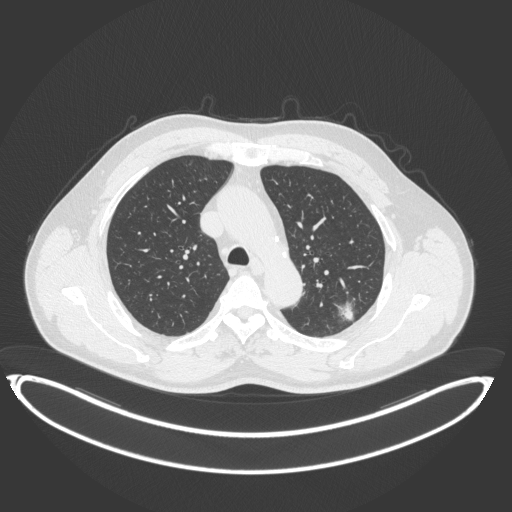
Chest CT, one axial slice; position 261 of 399 along the scan axis; reconstruction kernel B31f; 120 kVp; lung window (W 1500 / L -600 HU); 1 mm slice thickness; 512 × 512 image matrix. Male patient, age 58 years. From the clinical record (not read from this slice): clinical TNM (as recorded): T1c N0 M0; histopathological grade: G1-2.
Structures marked on this image (rectangle marked by the reading radiologist):
- lung tumour (recorded histology: adenocarcinoma): bounding box <334,298,361,325> (left, top, right, bottom; pixels)